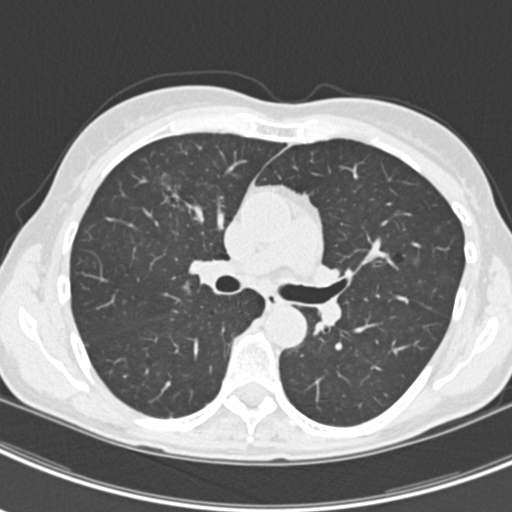
Axial slice from a low-dose chest CT screening exam, second screening round (one year after baseline), lung window (W 1500 / L -600 HU), 2 mm slice thickness, standard (soft-tissue) reconstruction kernel (B30f), 120 kVp. Female participant, aged 63 years at enrolment. Current smoker at enrolment.
- Lesion marked by an expert reader, bounding box <151,170,211,227> (left, top, right, bottom; pixels).
- The screening reader recorded 9 non-calcified nodules or masses ≥4 mm on this exam; which of them this box marks is not recorded.
- Official screen result: positive, other.